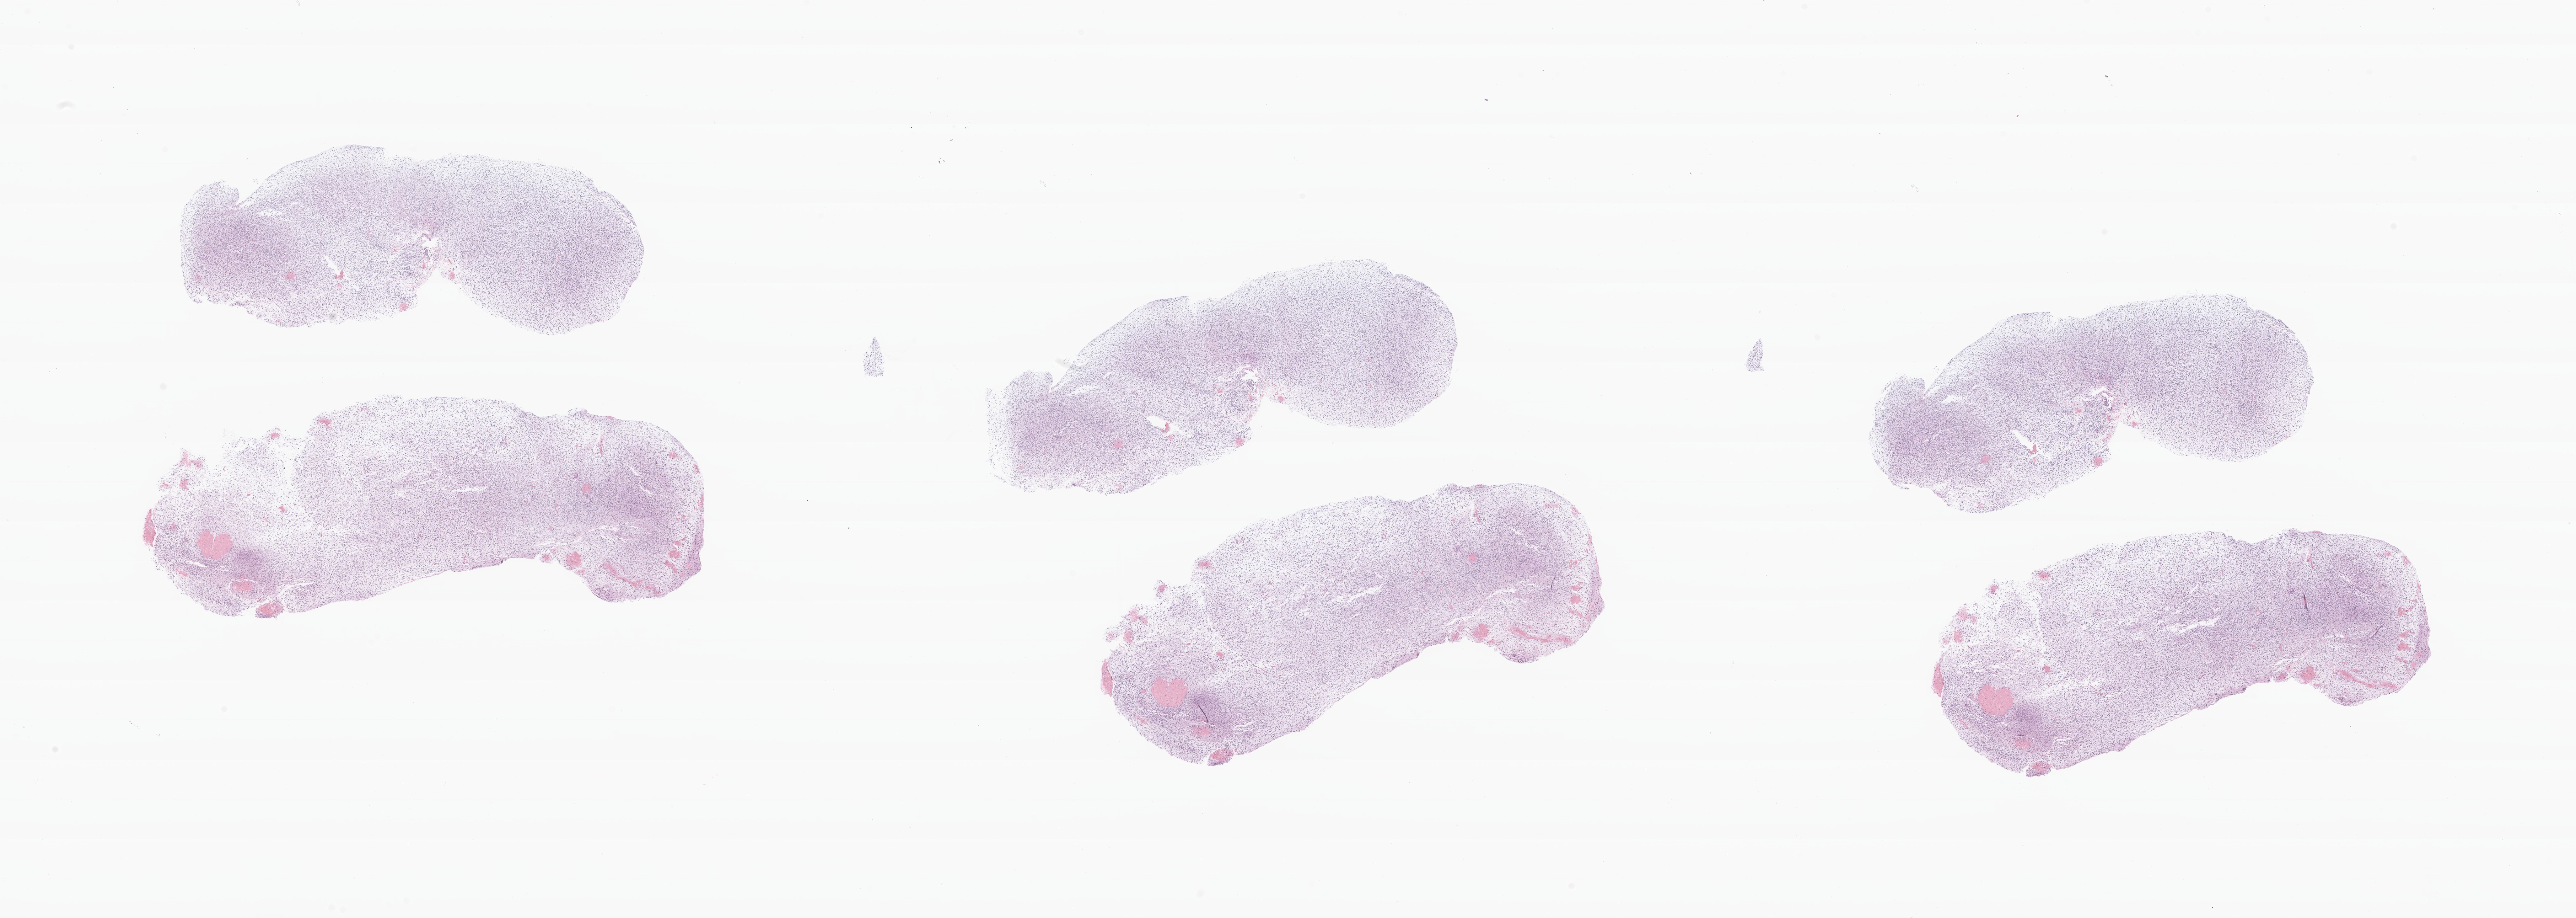
Whole-slide image, H&E stain of tumor tissue from the brain, whole scanned area (about 34.5 x 12.3 mm) shown as a low-resolution overview. Formalin-fixed, paraffin-embedded (FFPE) tissue. Patient: female, age 116 months (9 years 8 months).
Recorded diagnosis: Glioma, malignant.